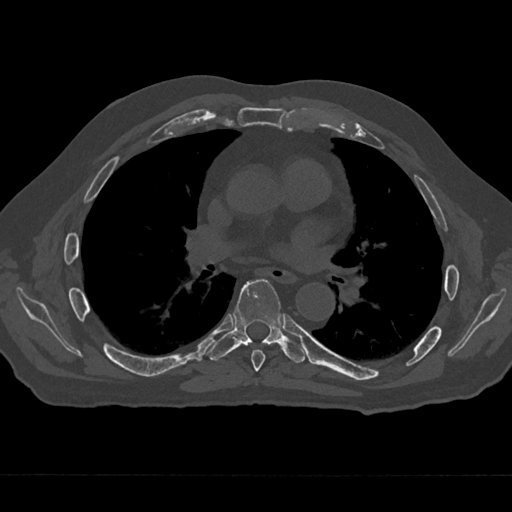
CT including the spine, one axial slice. Position 391 of 797 along the scan axis. Bone window (W 1800 / L 400 HU). 0.5 mm slice thickness. 512 × 512 image matrix, field of view 377 × 377 mm. Male patient, age 75 years. From the clinical record (not read from this slice): primary cancer: renal; vertebrae with lytic lesions (as recorded): T4.
Outlined on this slice (semi-automatically segmented with operator editing):
- T6 vertebra: bounding box [x1, y1, x2, y2] px = [251, 350, 266, 371]
- T7 vertebra: [208, 278, 305, 363]